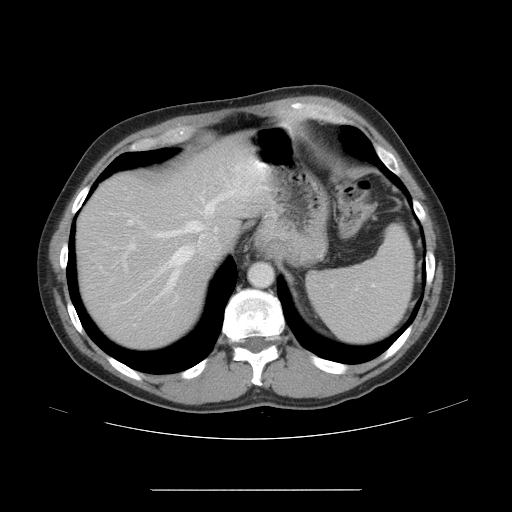
Contrast-enhanced abdominal CT, one axial slice. Slice 36 of 48 in the series (ordered by position). Reconstruction kernel STANDARD. 120 kVp. Intravenous contrast given. Soft-tissue window (W 400 / L 40 HU). 5 mm slice thickness. 512 × 512 image matrix, field of view 409 × 409 mm. Male patient, age 56 years. Case-level facts recorded for this patient, not image findings: diagnosis: colorectal cancer liver metastases, imaged before liver resection; multiple liver metastases: yes; largest metastasis: 1.8 cm.
Structures marked on this image (outlined manually by an expert reader):
- hepatic veins: bounding box [x1, y1, x2, y2] px = [149, 189, 237, 303]
- liver: [80, 140, 261, 342]
- planned liver remnant (the part of the liver to remain after resection): [80, 140, 262, 342]
- portal vein (with intrahepatic branches): [128, 219, 136, 250]